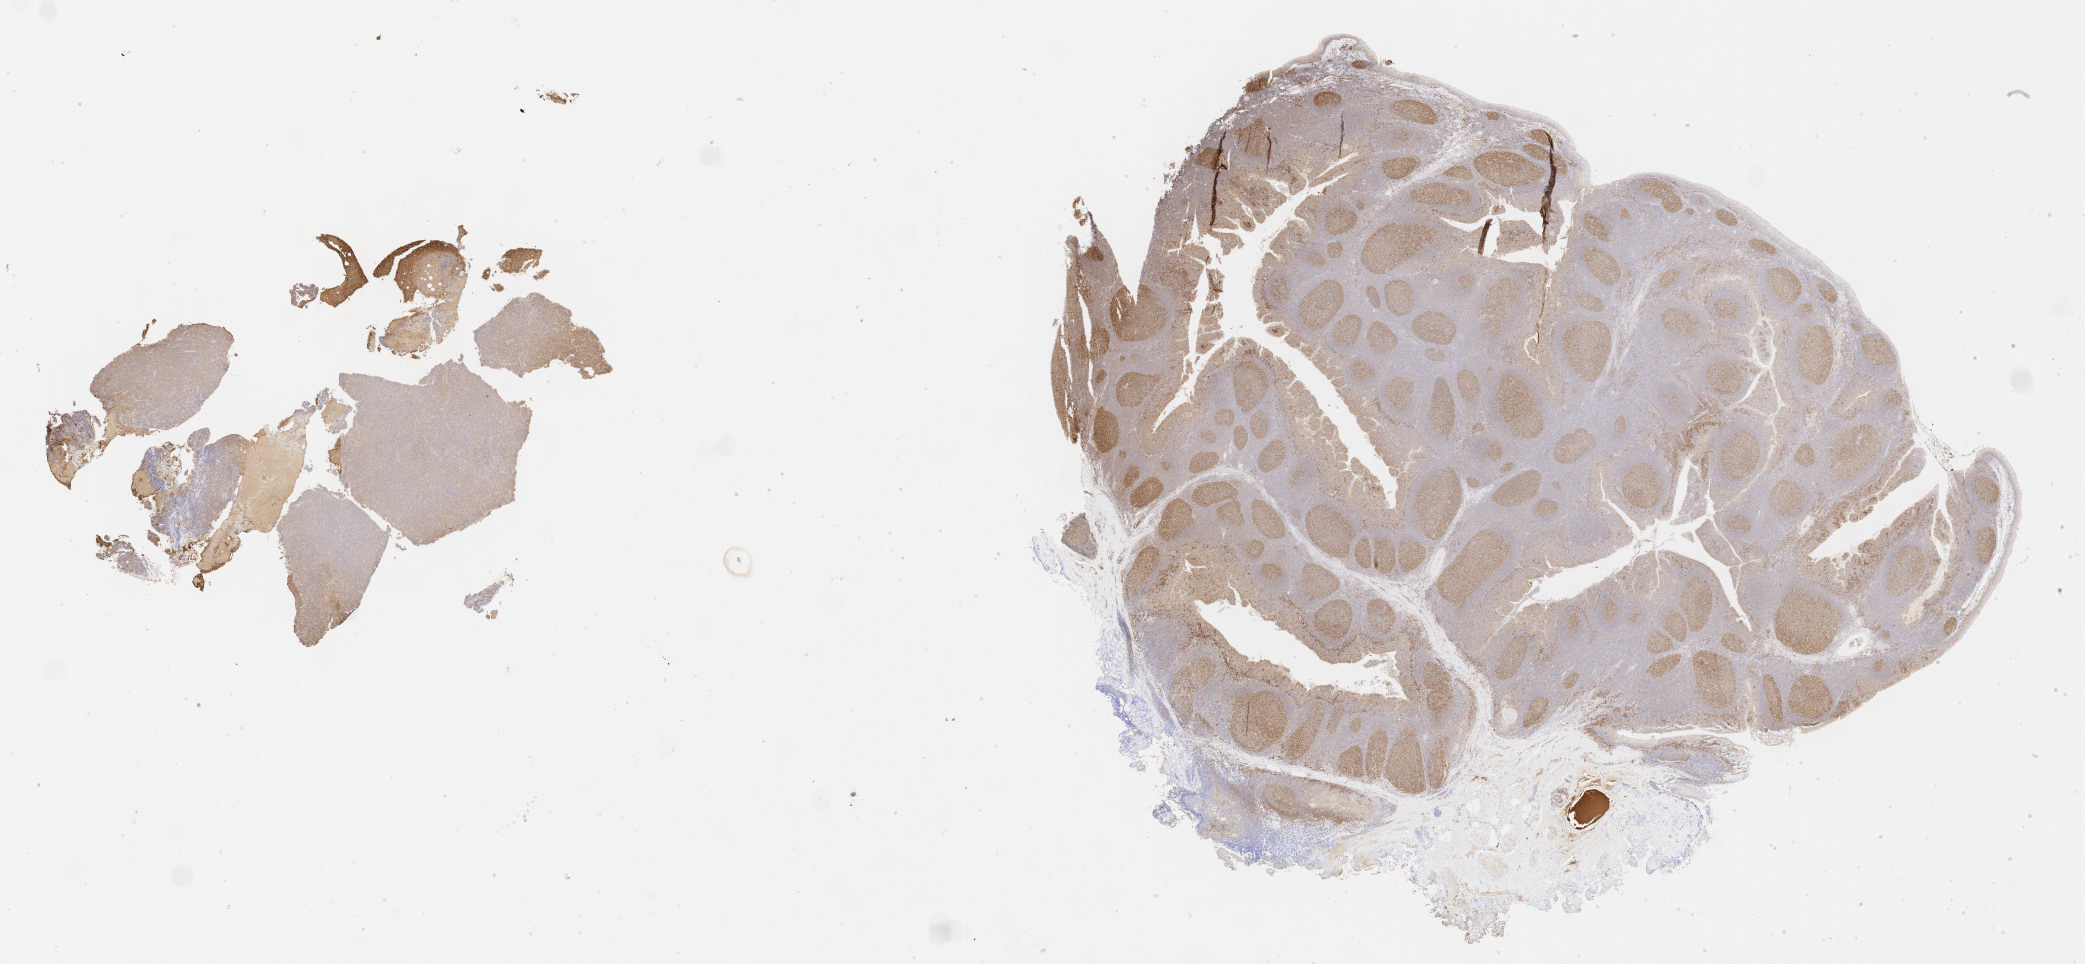
Immunohistochemistry (IHC) whole-slide image stained for BCL6, shown as a low-resolution overview of the whole scanned area (about 33.7 x 15.6 mm), specimen: tumor tissue, anatomic site: lymph node. Patient: female, 71 years old.
* histologic diagnosis: Diffuse large B-cell lymphoma, NOS